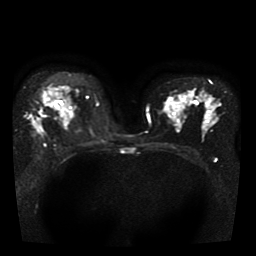
Breast MRI, one axial slice. Position 26 of 41 along the scan axis. Diffusion-weighted series; image 2 of 4 stored at this slice position (different b-values; order by instance number). 1.5 T. 5 mm slice thickness. 256 × 256 image matrix, field of view 330 × 330 mm. Female patient.
Annotated regions visible in this slice (manually delineated by an expert):
- tumour on diffusion-weighted imaging: bounding box [x1, y1, x2, y2] px = [33, 93, 48, 136]